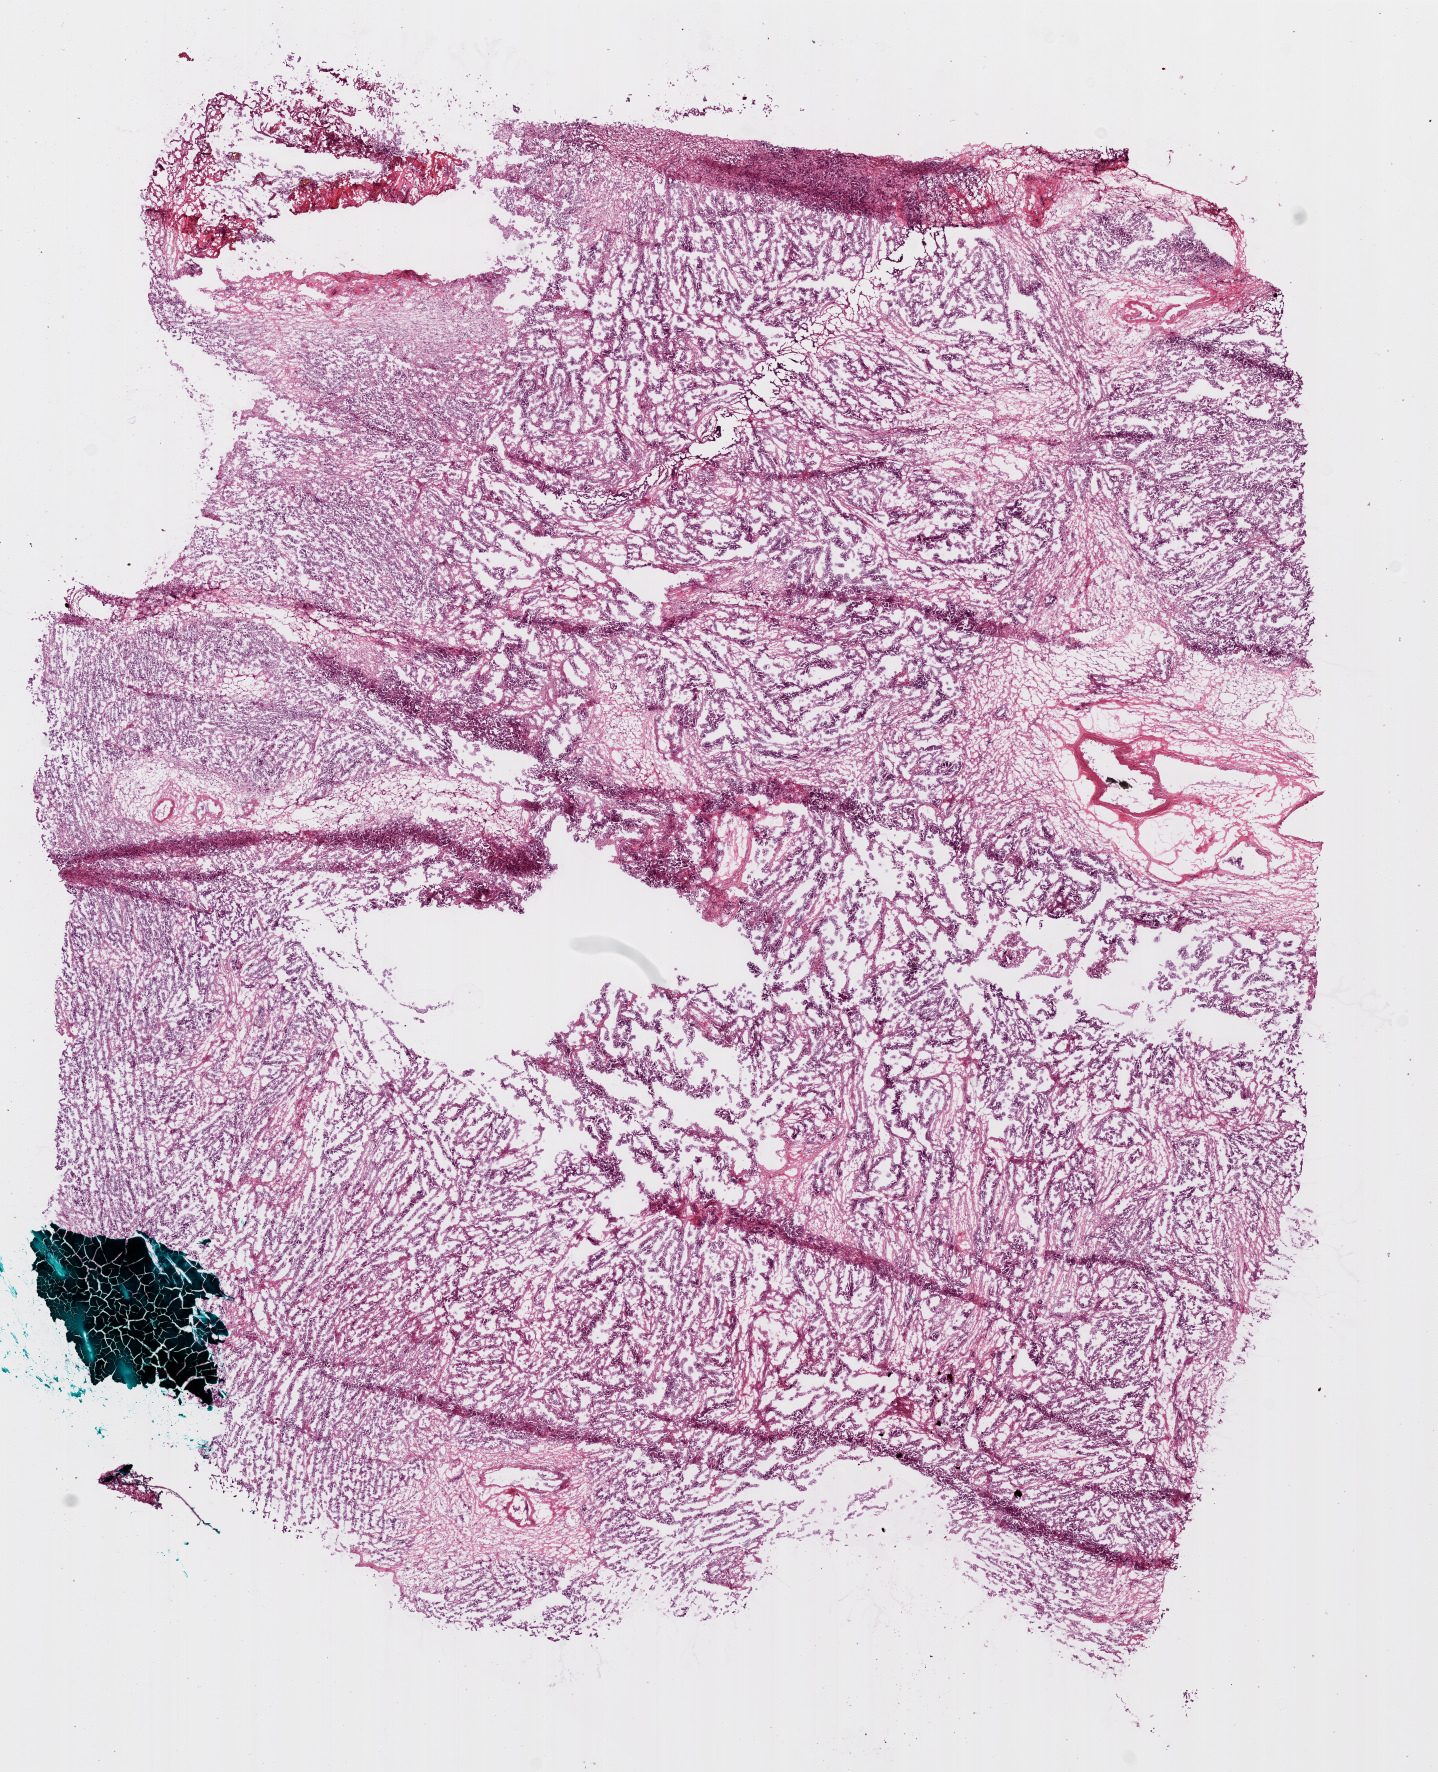
H&E whole-slide image — whole scanned area (about 11.6 x 14.3 mm, slide scanned at 20x) shown as a low-resolution overview; frozen section; ovary, primary tumour sample. Female patient; age at initial diagnosis 40 years. Histologic grade: G3 (poorly differentiated). Slide review estimates, as recorded: tumour cells 90%, tumour nuclei 98%, normal cells 0%, stromal cells 10%, necrosis 0%.
* FIGO stage: IV
* diagnosis: Serous cystadenocarcinoma, NOS